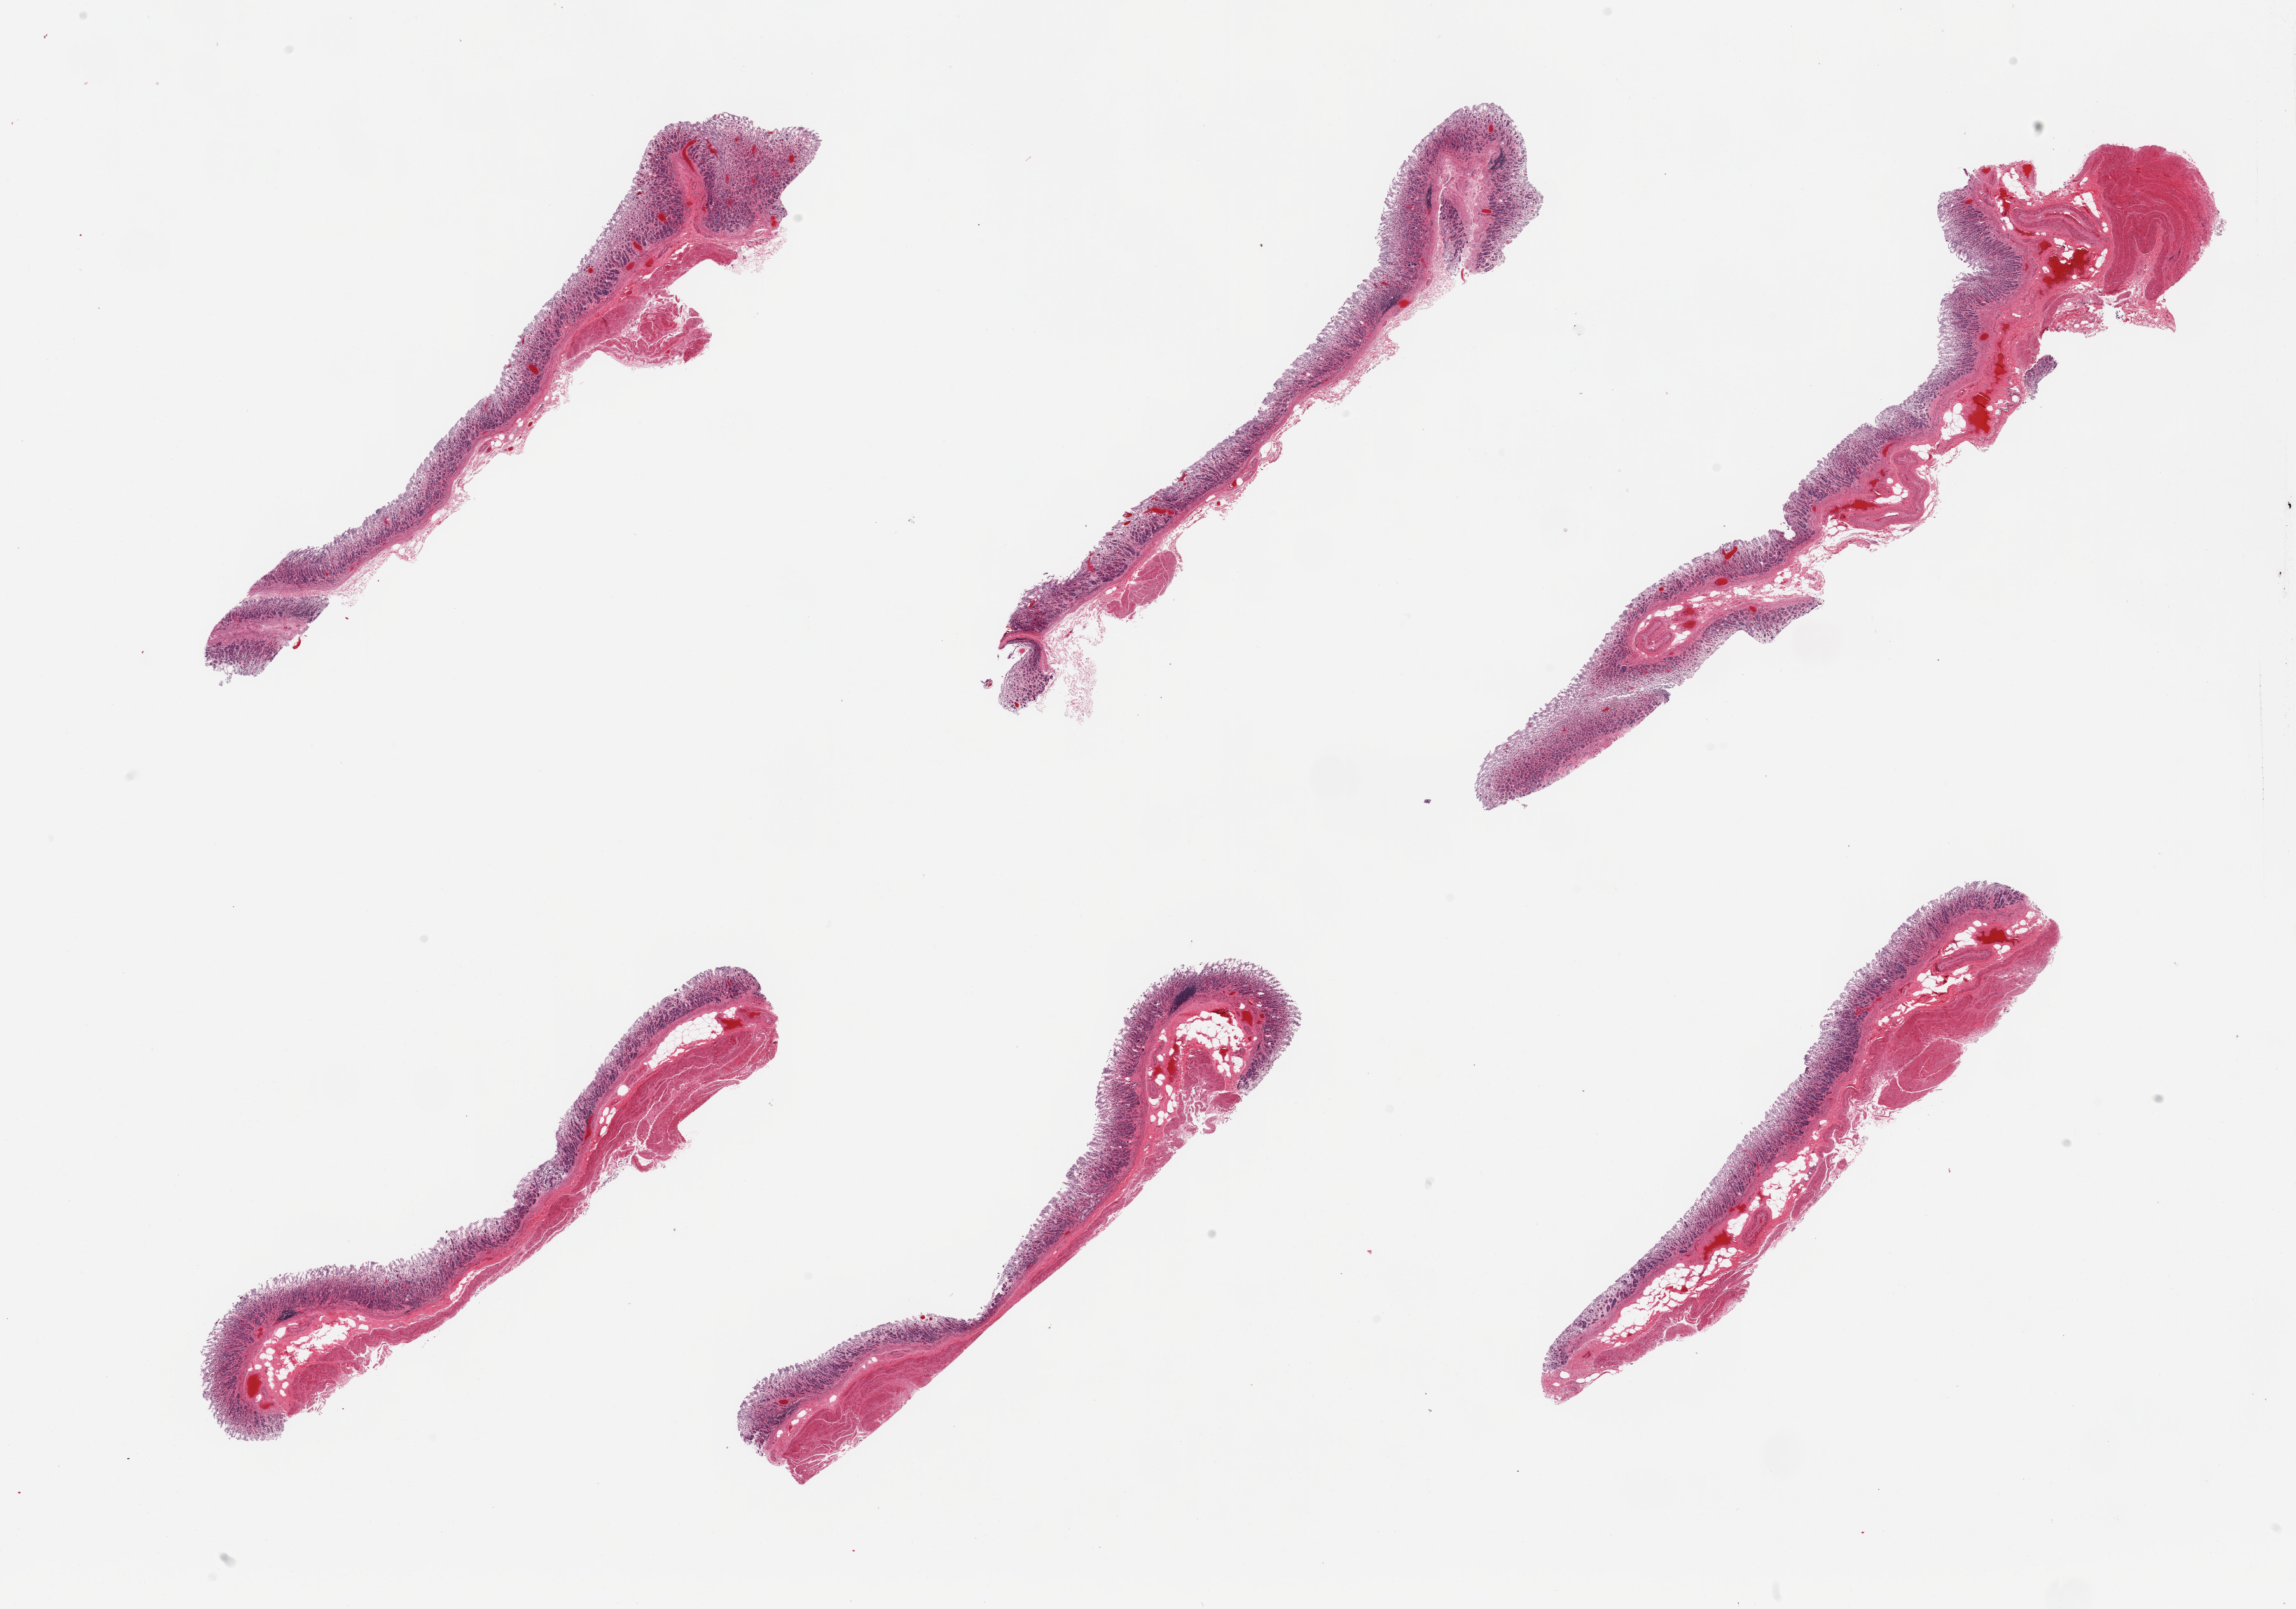
Whole-slide image, H&E stain, a low-resolution overview of the entire scanned area, about 28.5 x 20.0 mm (acquisition: 20x scan); PAXgene-fixed, paraffin-embedded tissue; section of stomach (target tissue); tissue donor sample. Male donor.
Reviewer comment on this tissue sample: 6 pieces; mostly mucosa and submucosa; some sections include muscularis.